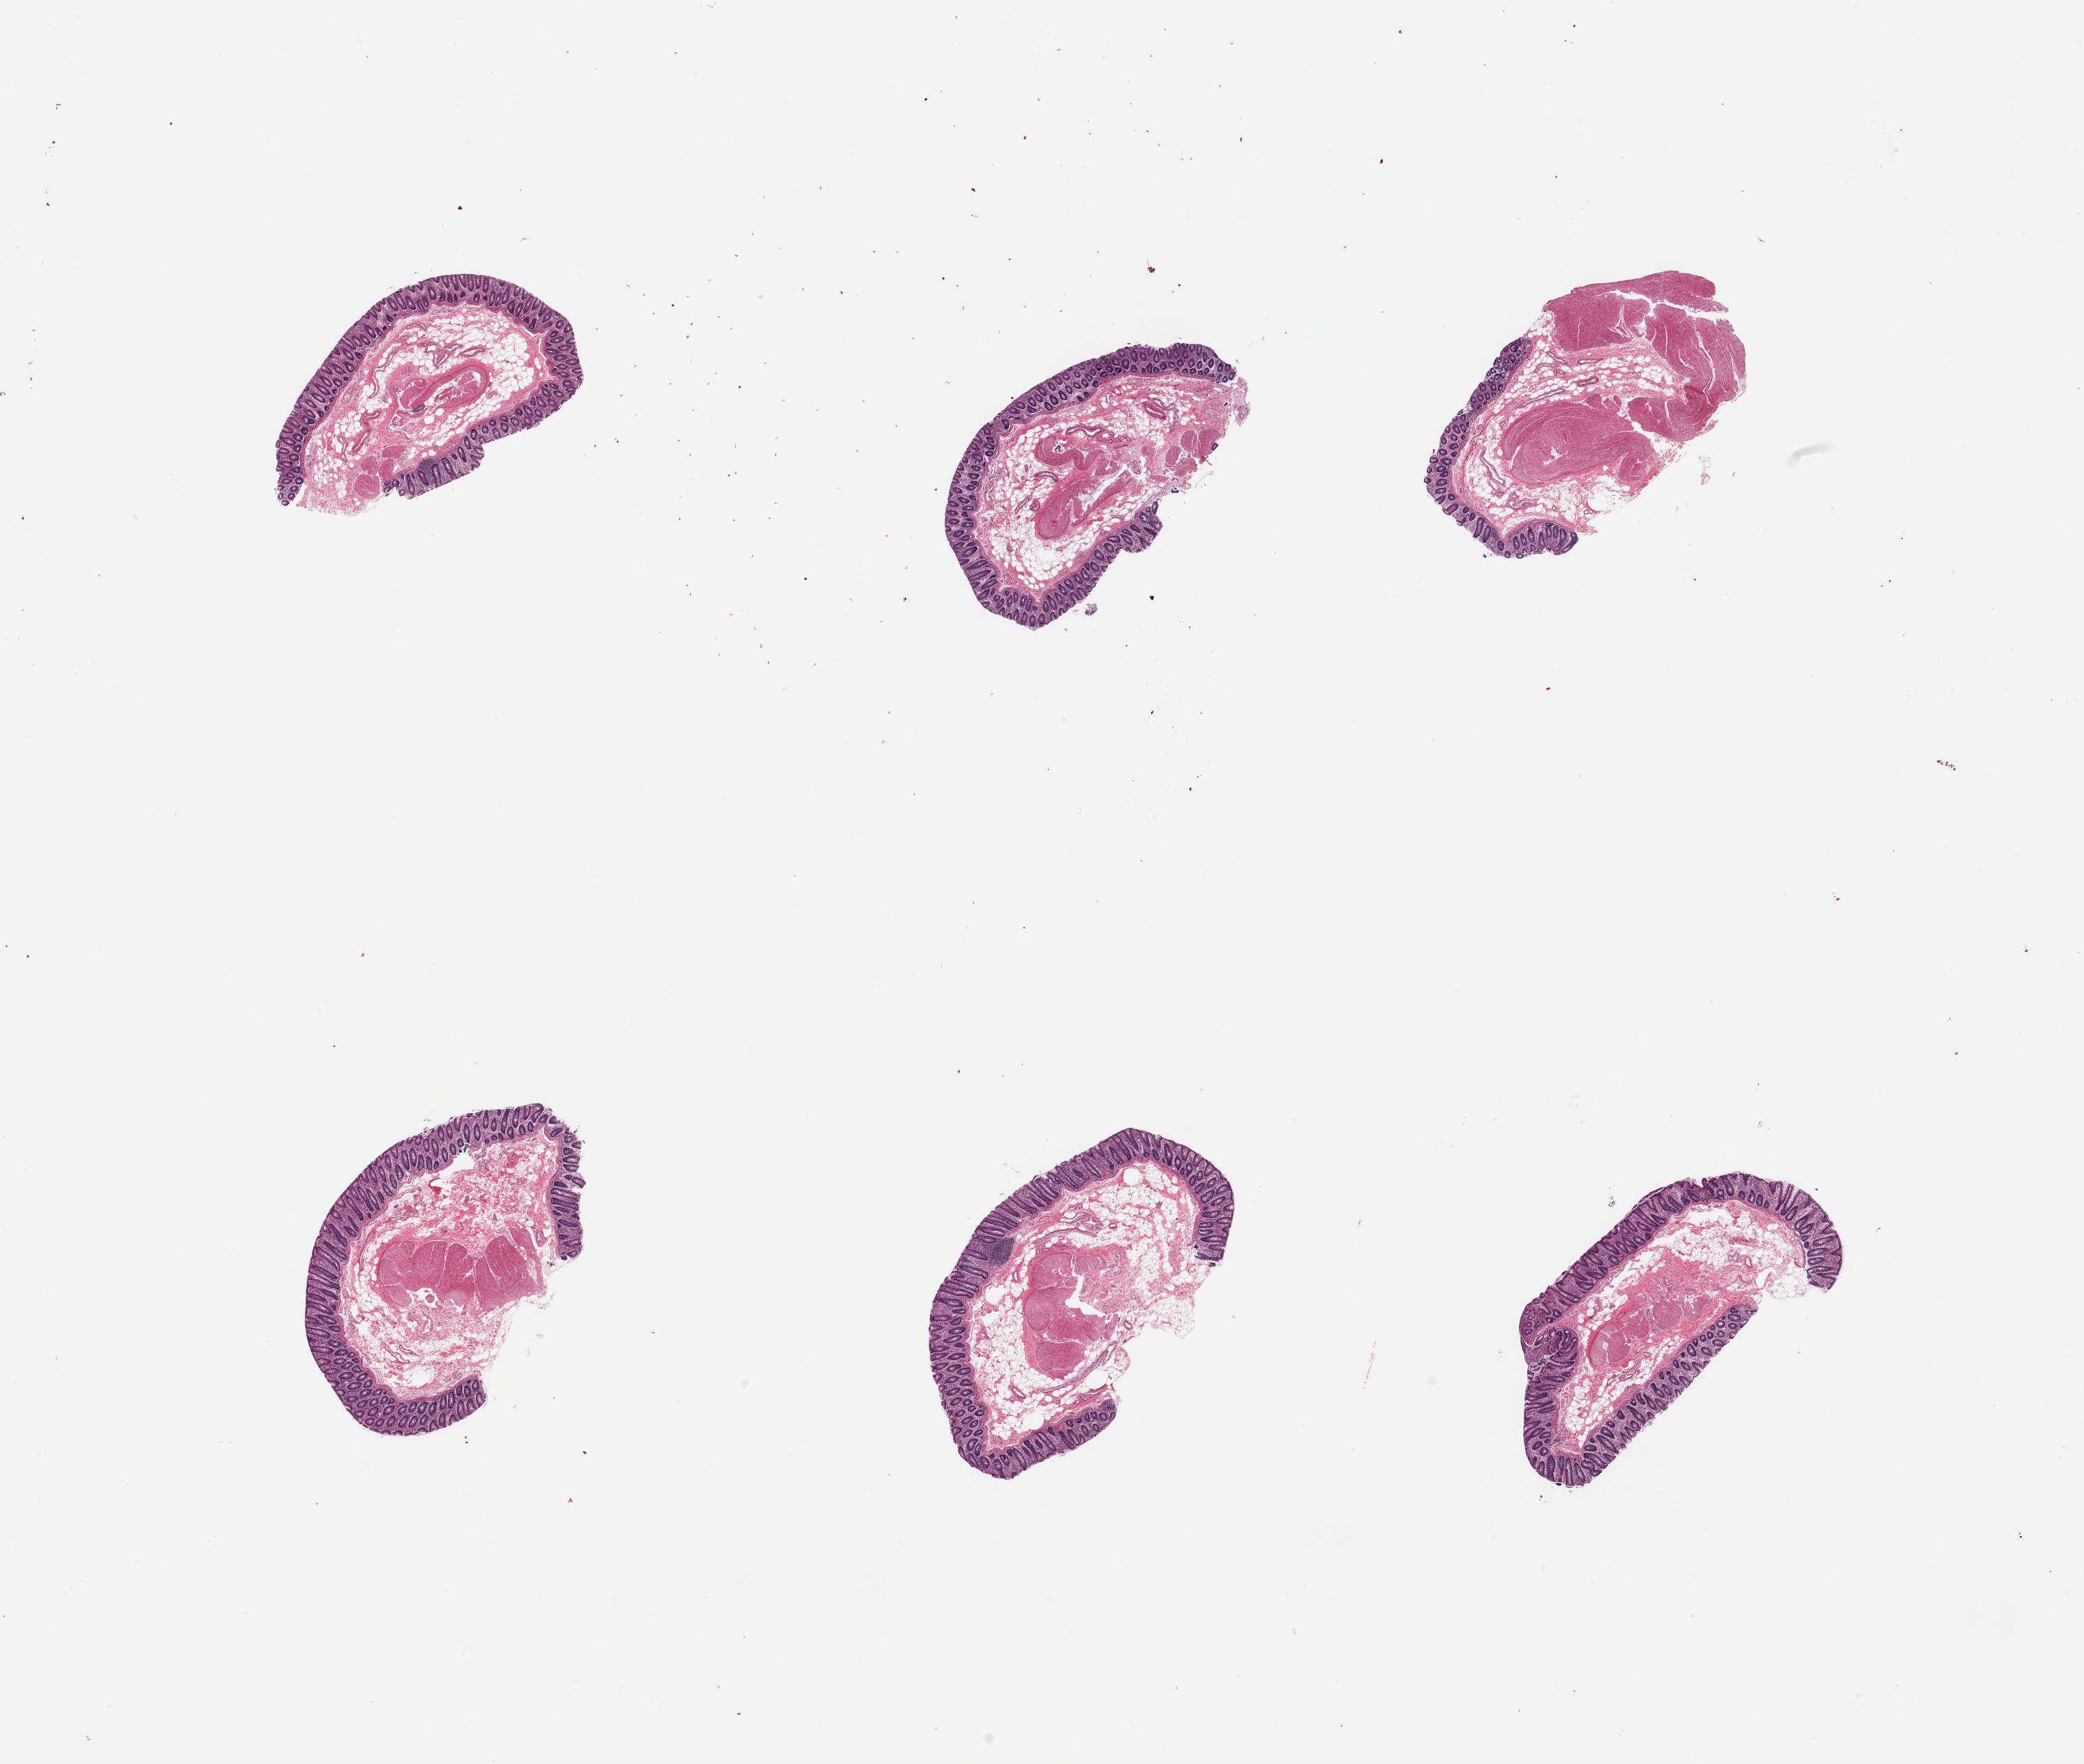
H&E whole-slide image, brightfield, whole scanned area (about 23.6 x 20.0 mm) shown as a low-resolution overview, PAXgene-fixed paraffin-embedded (PFPE) section, sampled site (target tissue): sigmoid colon, donor tissue sample. Donor: male.
Review note (as recorded): 6 pieces; muscularis is ~50% total tissue, rest is mucosa/fat.